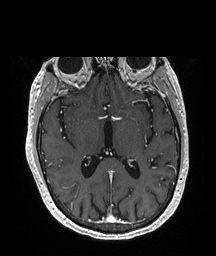
Brain MRI from a brain-tumour surgery series, one axial slice. Slice 110 of 208 in the series (ordered by position). T1-weighted post-contrast. 216 × 256 image matrix. Case-level facts recorded for this patient, not image findings: histopathology: Glioblastoma; WHO grade: 4; IDH mutation: no; tumour location: Right Temporal.
Annotated regions visible in this slice (outlined manually by an expert reader):
- tumour: bounding box <66,184,70,186> (left, top, right, bottom; pixels)